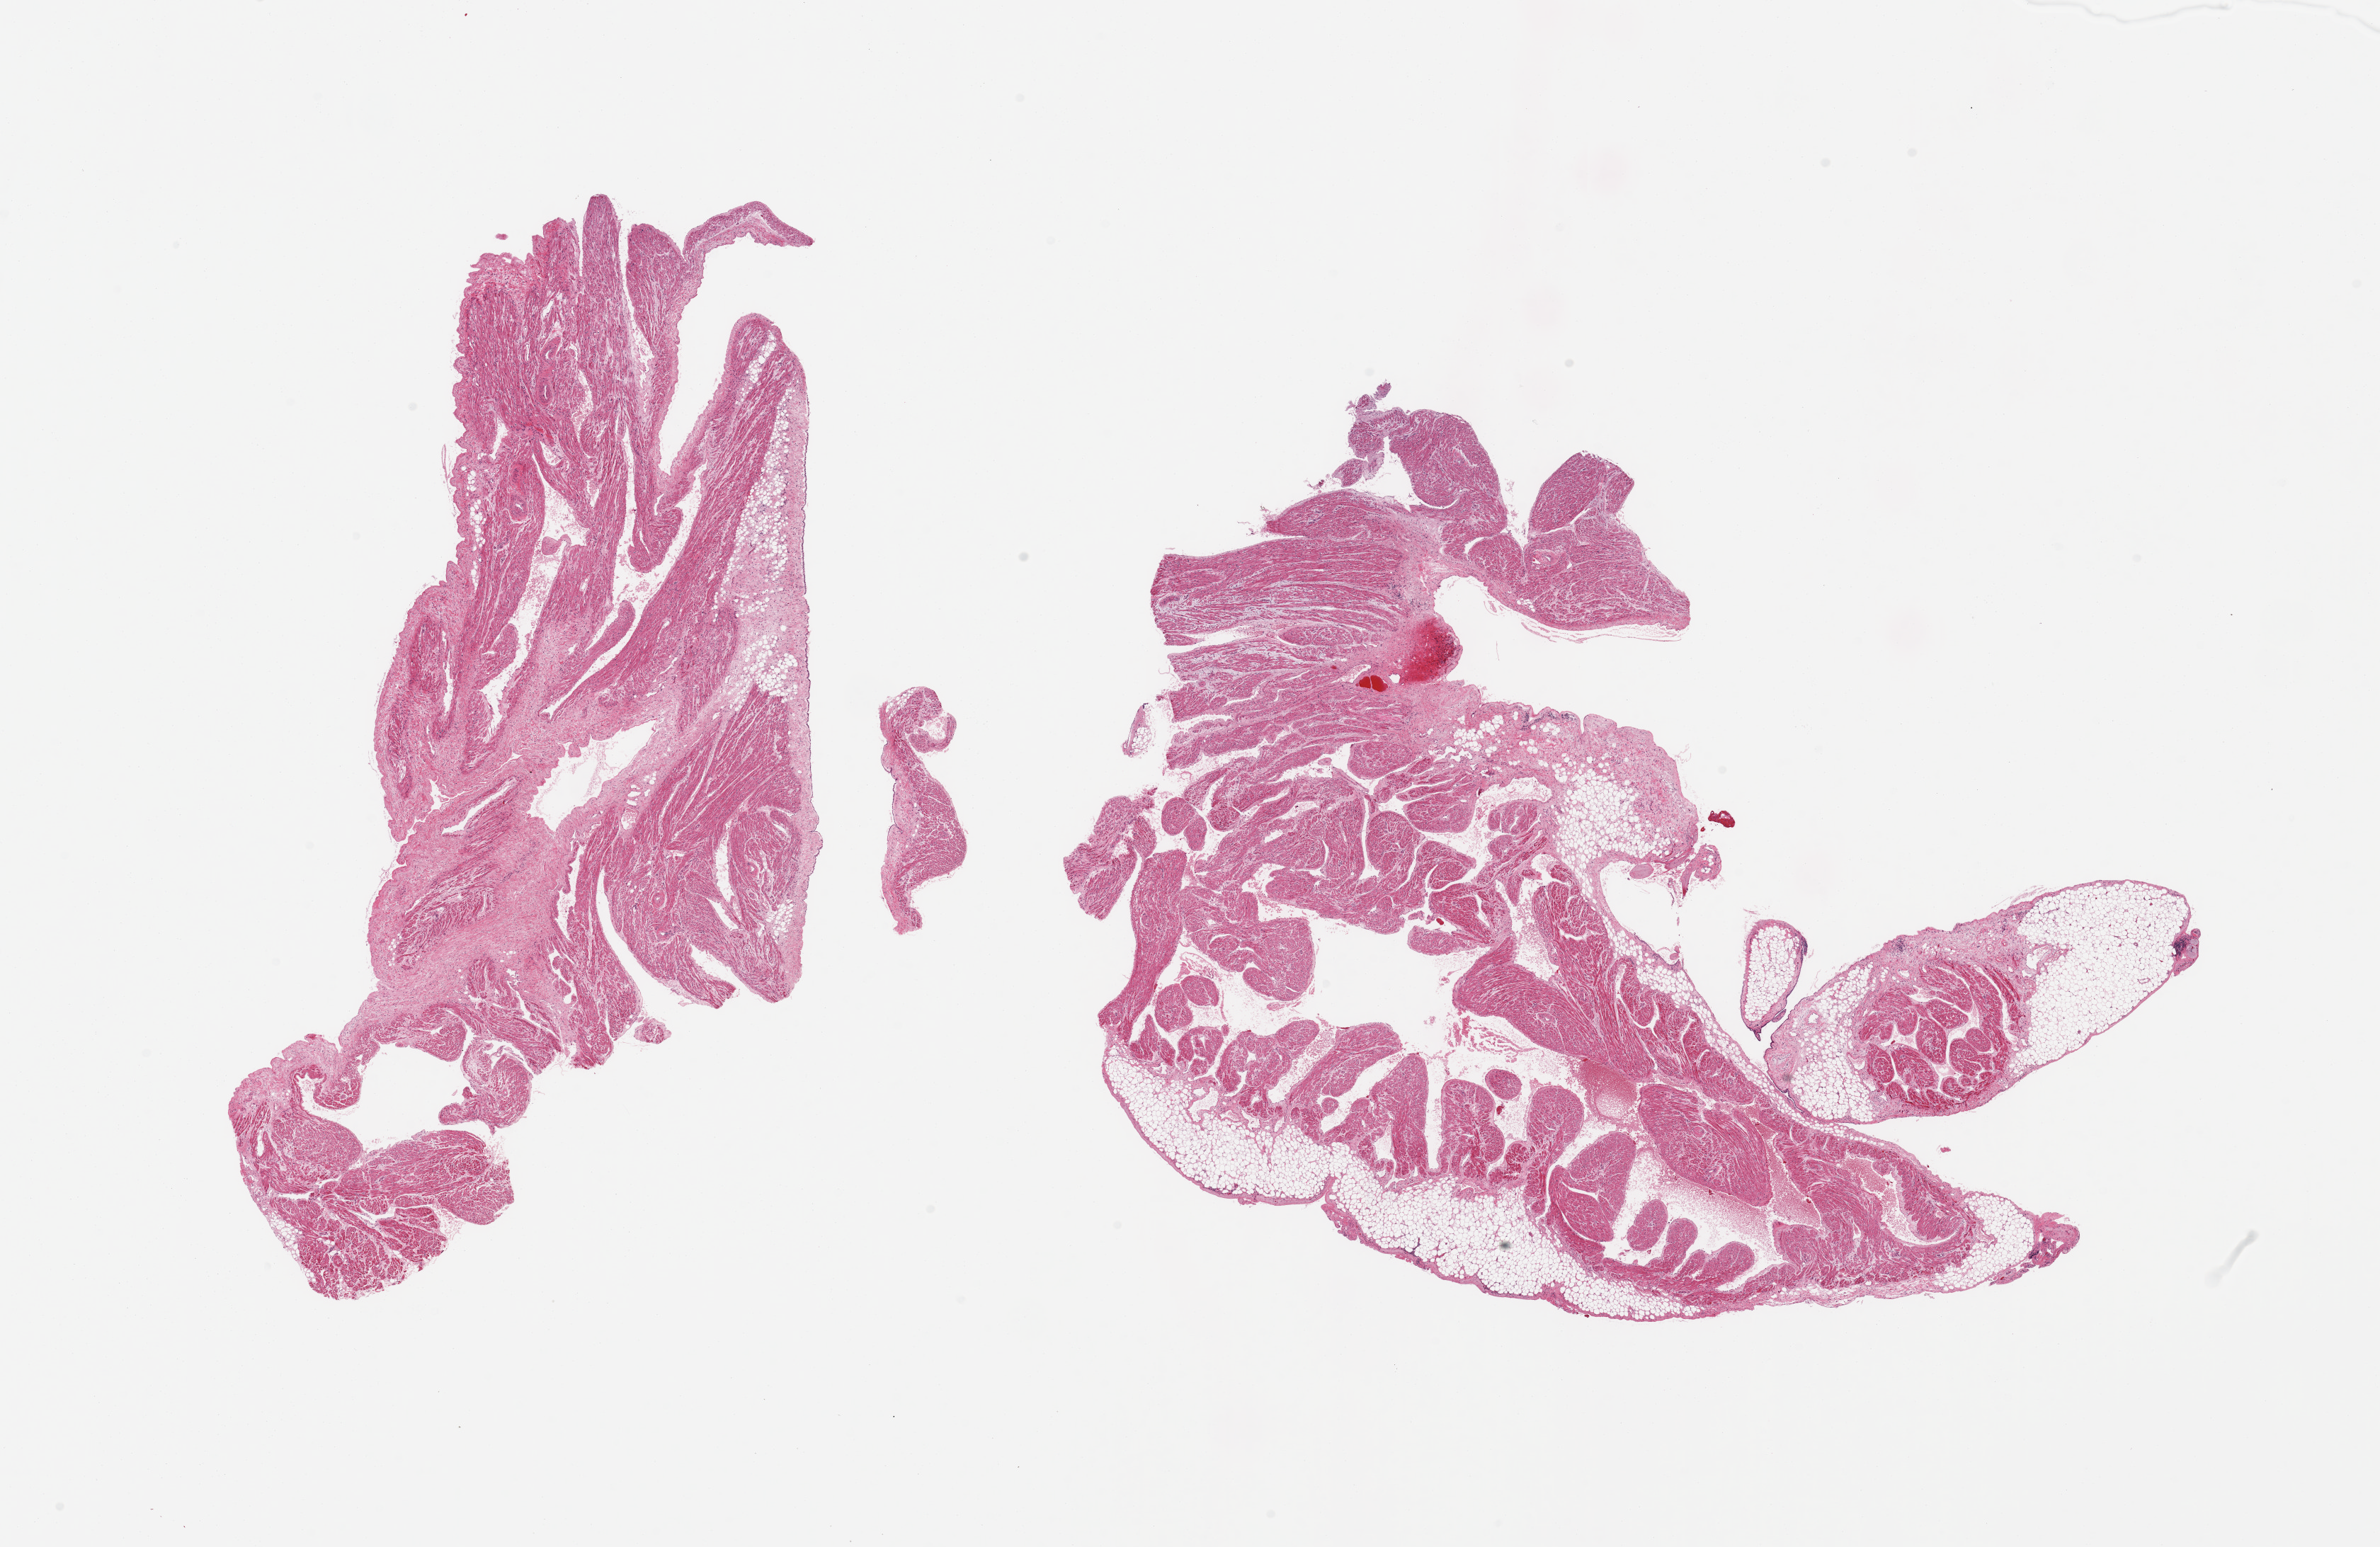
Digitized haematoxylin and eosin-stained section, a low-resolution overview of the entire scanned area, about 26.6 x 17.3 mm; PAXgene-fixed paraffin-embedded (PFPE) section; section of auricular appendage (target tissue); donor tissue sample.
Review note (as recorded): 2 pieces; 30% fibroadipose content.